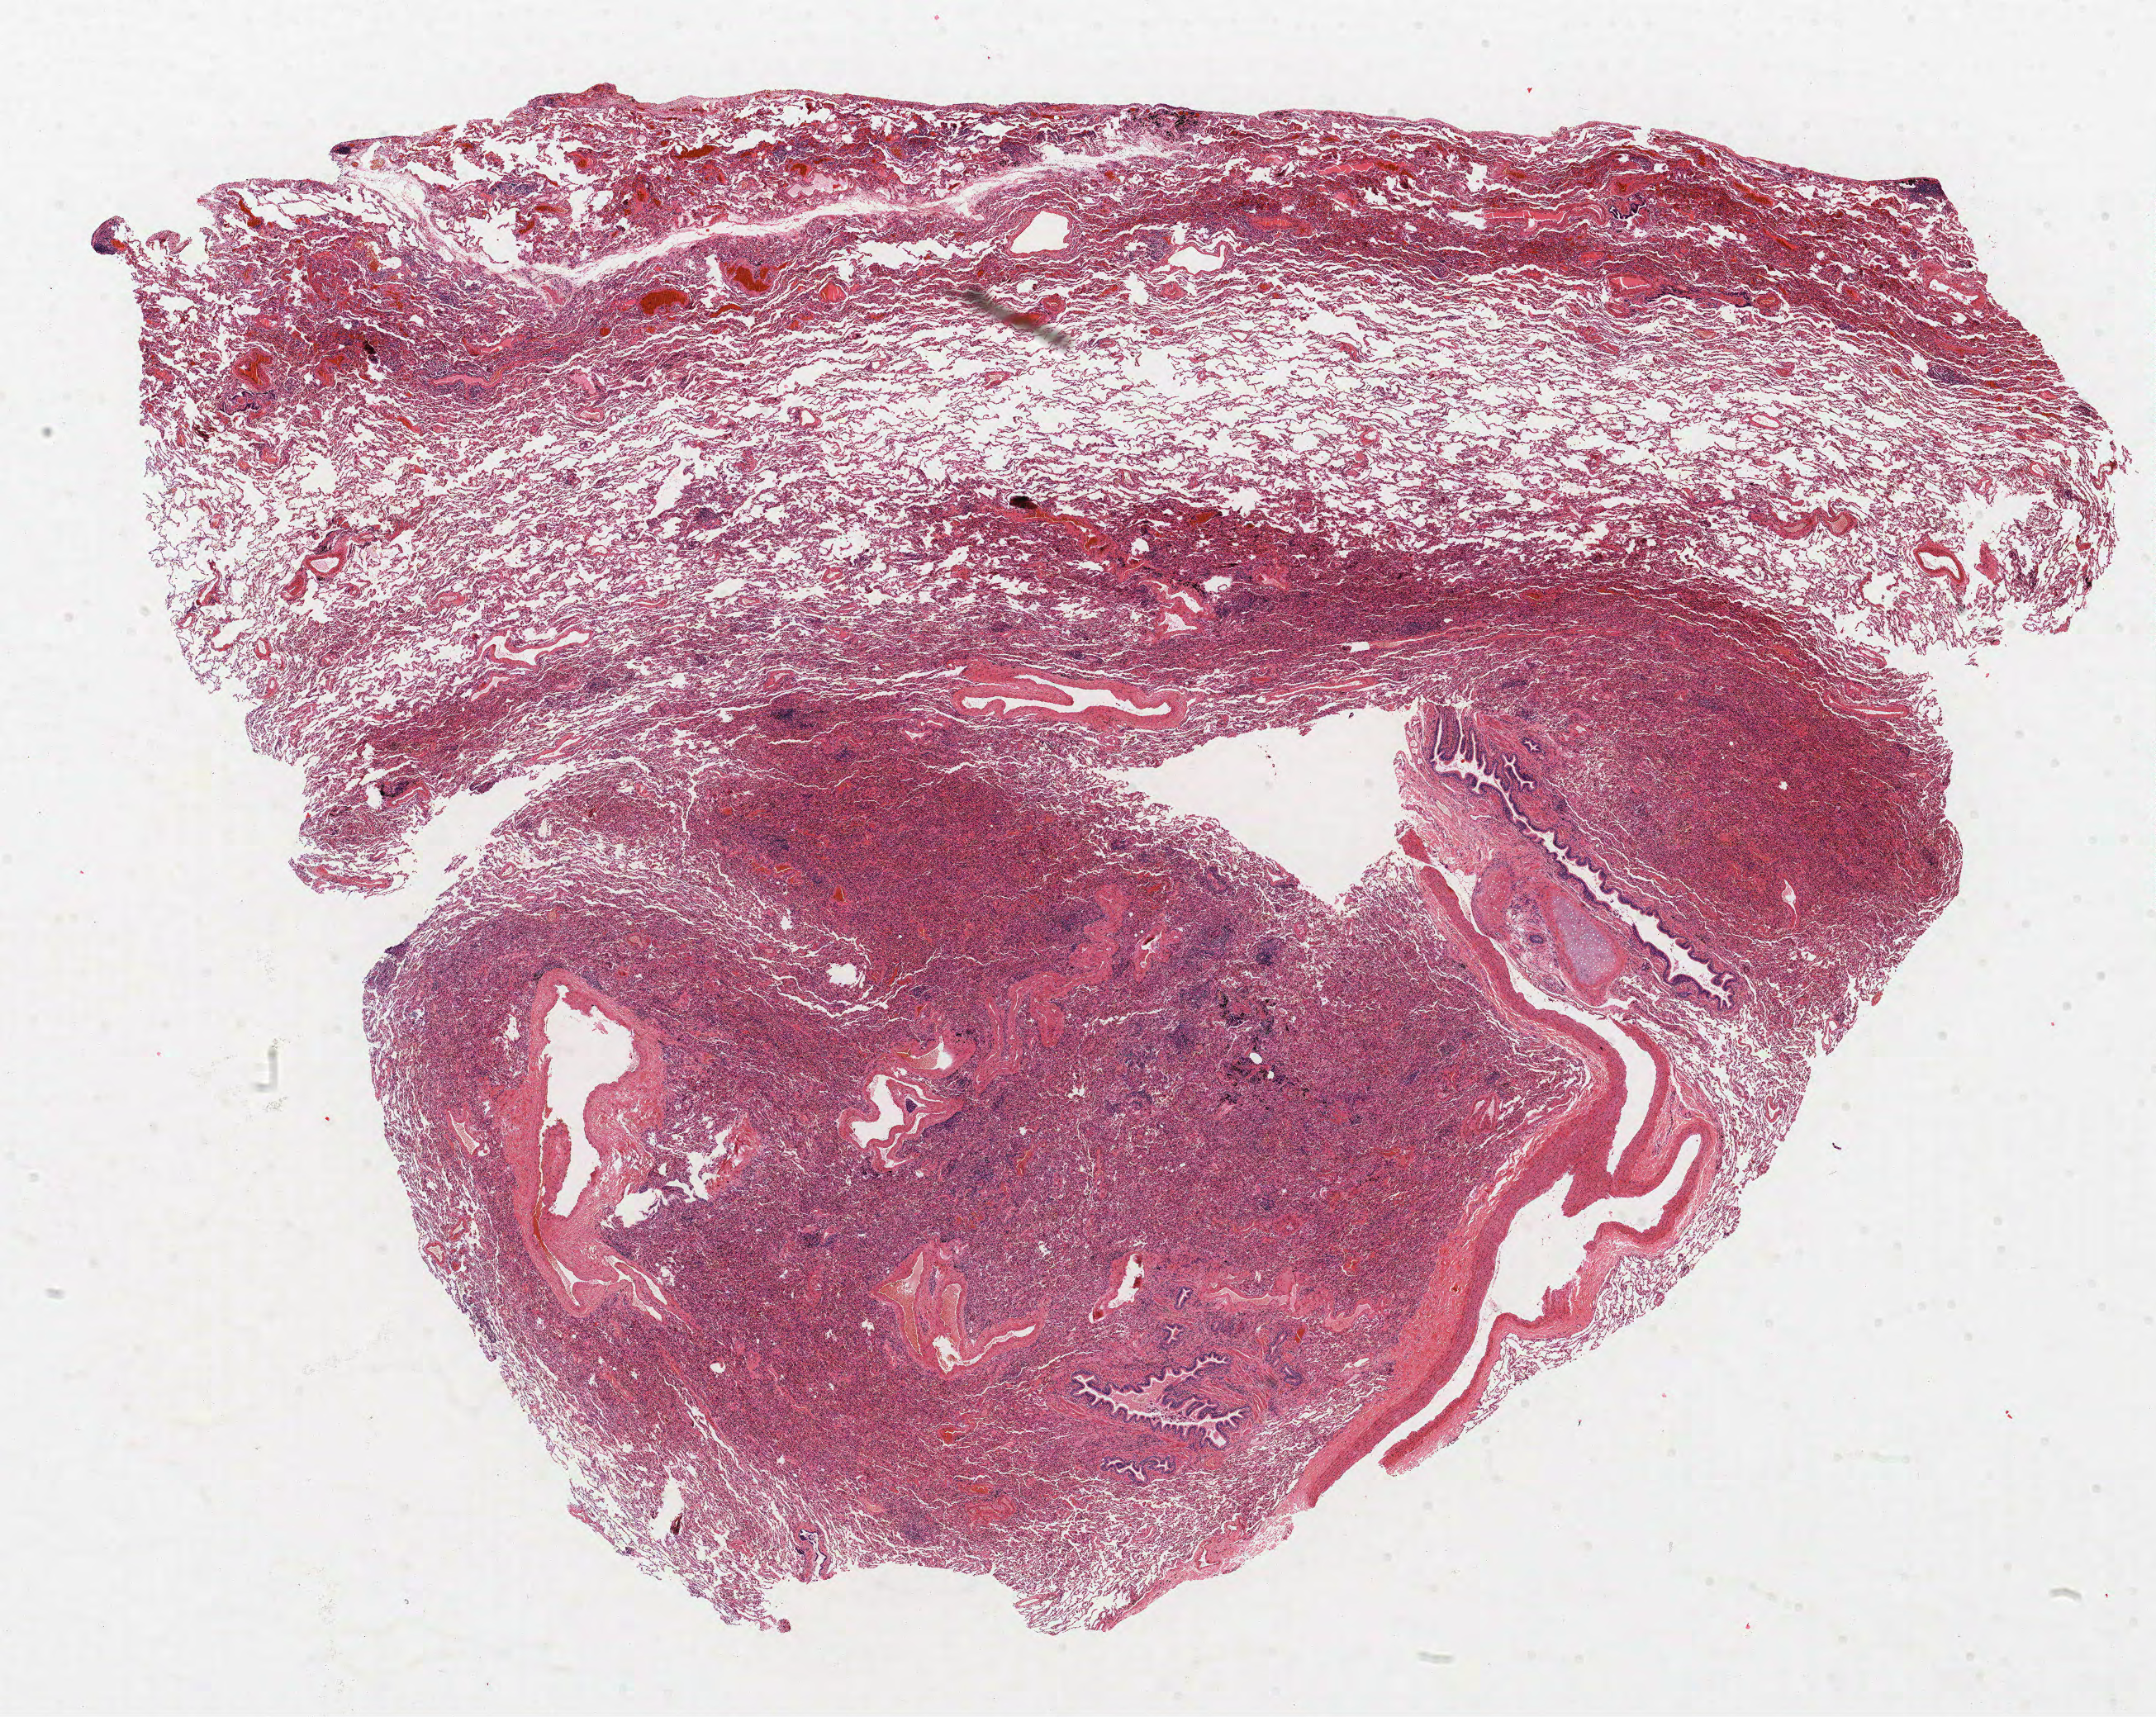
Whole-slide histology image, H&E-stained — a low-resolution overview of the entire scanned area, about 20.9 x 16.6 mm (slide scanned at 40x), formalin-fixed paraffin-embedded (FFPE) section, lung tissue. Male patient, aged 56 at enrolment. Former smoker at enrolment. Grade: poorly differentiated (G3).
ICD-O-3 topography: upper lobe of lung (C34.1). Stage (AJCC 6th edition): IA. Primary tumour location (clinical record): right upper lobe. Tumour size (pathology): 12 mm. Participant's lung-cancer diagnosis: Adenocarcinoma, NOS (ICD-O-3 8140/3).